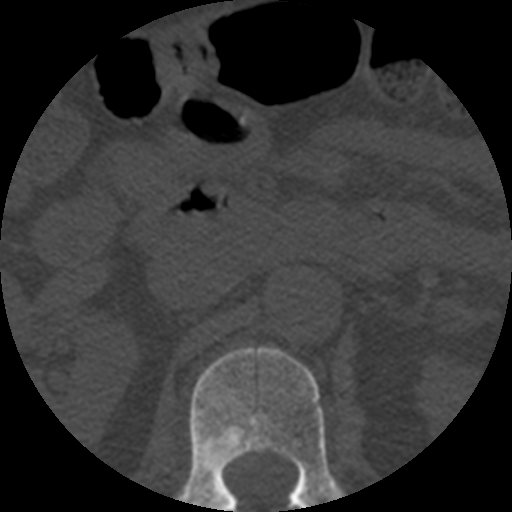
CT including the spine, one axial slice. Position 187 of 508 along the scan axis. Reconstruction kernel STANDARD. Bone window (W 1800 / L 400 HU). 1.25 mm slice thickness. 512 × 512 image matrix, field of view 160 × 160 mm. Patient age 57 years. Case-level facts recorded for this patient, not image findings: primary cancer: prostate.
Annotated regions visible in this slice (semi-automatically segmented with operator editing):
- L1 vertebra: bounding box <176,347,342,512> (left, top, right, bottom; pixels)